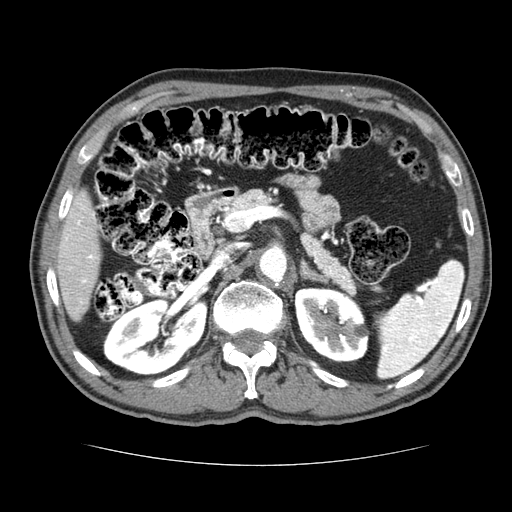
Contrast-enhanced abdominal CT (liver protocol), one axial slice. Slice 35 of 79 in the series (ordered by position). Reconstruction kernel STANDARD. 120 kVp. Soft-tissue window (W 400 / L 40 HU). 2.5 mm slice thickness. 512 × 512 image matrix. Case-level facts recorded for this patient, not image findings: diagnosis: hepatocellular carcinoma (patient treated with transarterial chemoembolisation; whether this scan precedes or follows treatment is not stated here); TNM stage (as recorded): Stage-I; Child-Pugh class: A; tumour nodularity: uninodular.
Outlined on this slice (semi-automatic segmentation, software-assisted and operator-edited):
- liver parenchyma outside the tumour (the mass and vessels are separate outlines, so this box may not span the whole liver): bounding box (x1, y1, x2, y2) in pixels: (56, 189, 100, 320)
- liver vessels: (65, 207, 95, 283)